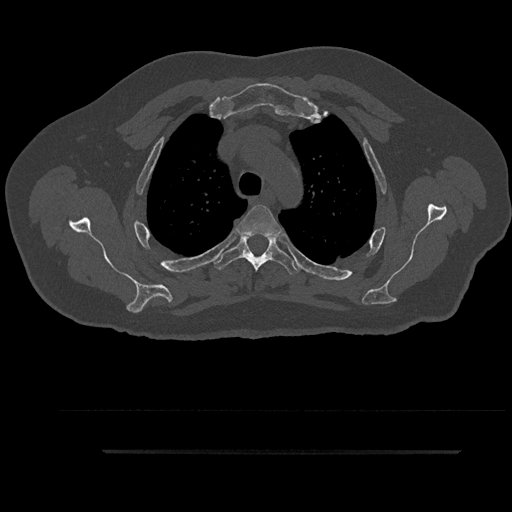
CT including the spine, one axial slice. Position 691 of 797 along the scan axis. Reconstruction kernel Br40s/3. 120 kVp. Bone window (W 1800 / L 400 HU). 0.5 mm slice thickness. 512 × 512 image matrix, field of view 432 × 432 mm. Patient: male, 63 years. Case-level facts recorded for this patient, not image findings: primary cancer: renal.
Annotated regions visible in this slice (semi-automatically segmented with operator editing):
- T3 vertebra: bounding box [x1, y1, x2, y2] px = [236, 205, 282, 238]
- T4 vertebra: [213, 235, 300, 274]